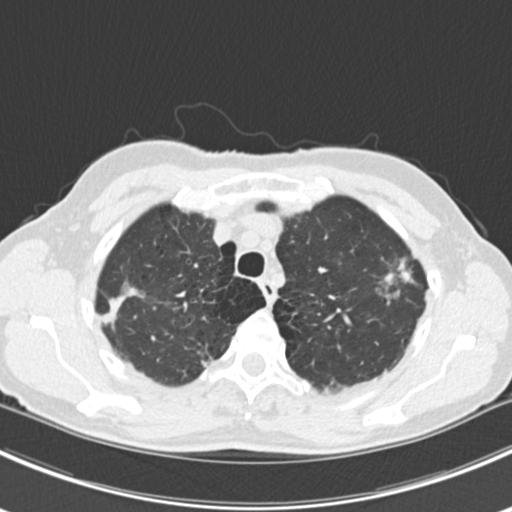
Axial slice from a low-dose chest CT screening exam; baseline annual screen; lung window (W 1500 / L -600 HU); 2 mm slice thickness; standard (soft-tissue) reconstruction kernel (B30f); slice 40 of 224 in the series. Female, age 63 years at enrolment. Current smoker at enrolment.
Lesion marked by an expert reader, box from (x=365, y=248) to (x=429, y=313) px. The screening reader recorded 10 non-calcified nodules or masses ≥4 mm on this exam (right lower lobe, right lower lobe, left lower lobe, left lower lobe, right middle lobe, right lower lobe, left lower lobe, left upper lobe, right upper lobe, left upper lobe); which of them this box marks is not recorded. Participant outcome: lung cancer diagnosed 751 days after this screen (after the third annual screen) — bronchiolo-alveolar adenocarcinoma, NOS, right upper lobe, right middle lobe, right lower lobe, left upper lobe, left lower lobe, moderately differentiated (G2), stage IV (AJCC 6th edition).